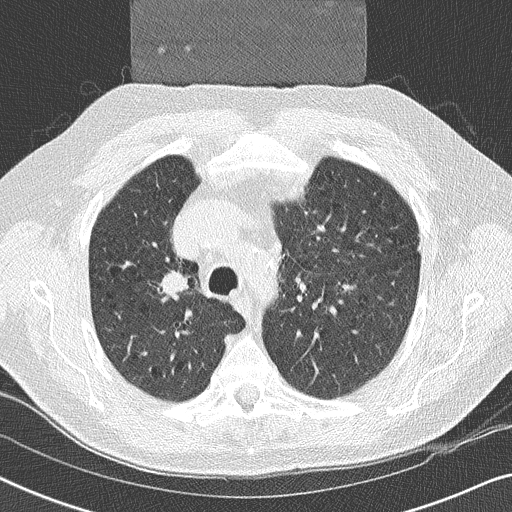
Low-dose screening chest CT, one axial slice. Position 177 of 252 along the scan axis. 120 kVp. Lung window (W 1500 / L -600 HU). 2 mm slice thickness. 512 × 512 image matrix.
Outlined on this slice (manually delineated by an expert):
- lesion 1 (tumor, upper lobe of right lung): bounding box <163,272,189,296> (left, top, right, bottom; pixels)